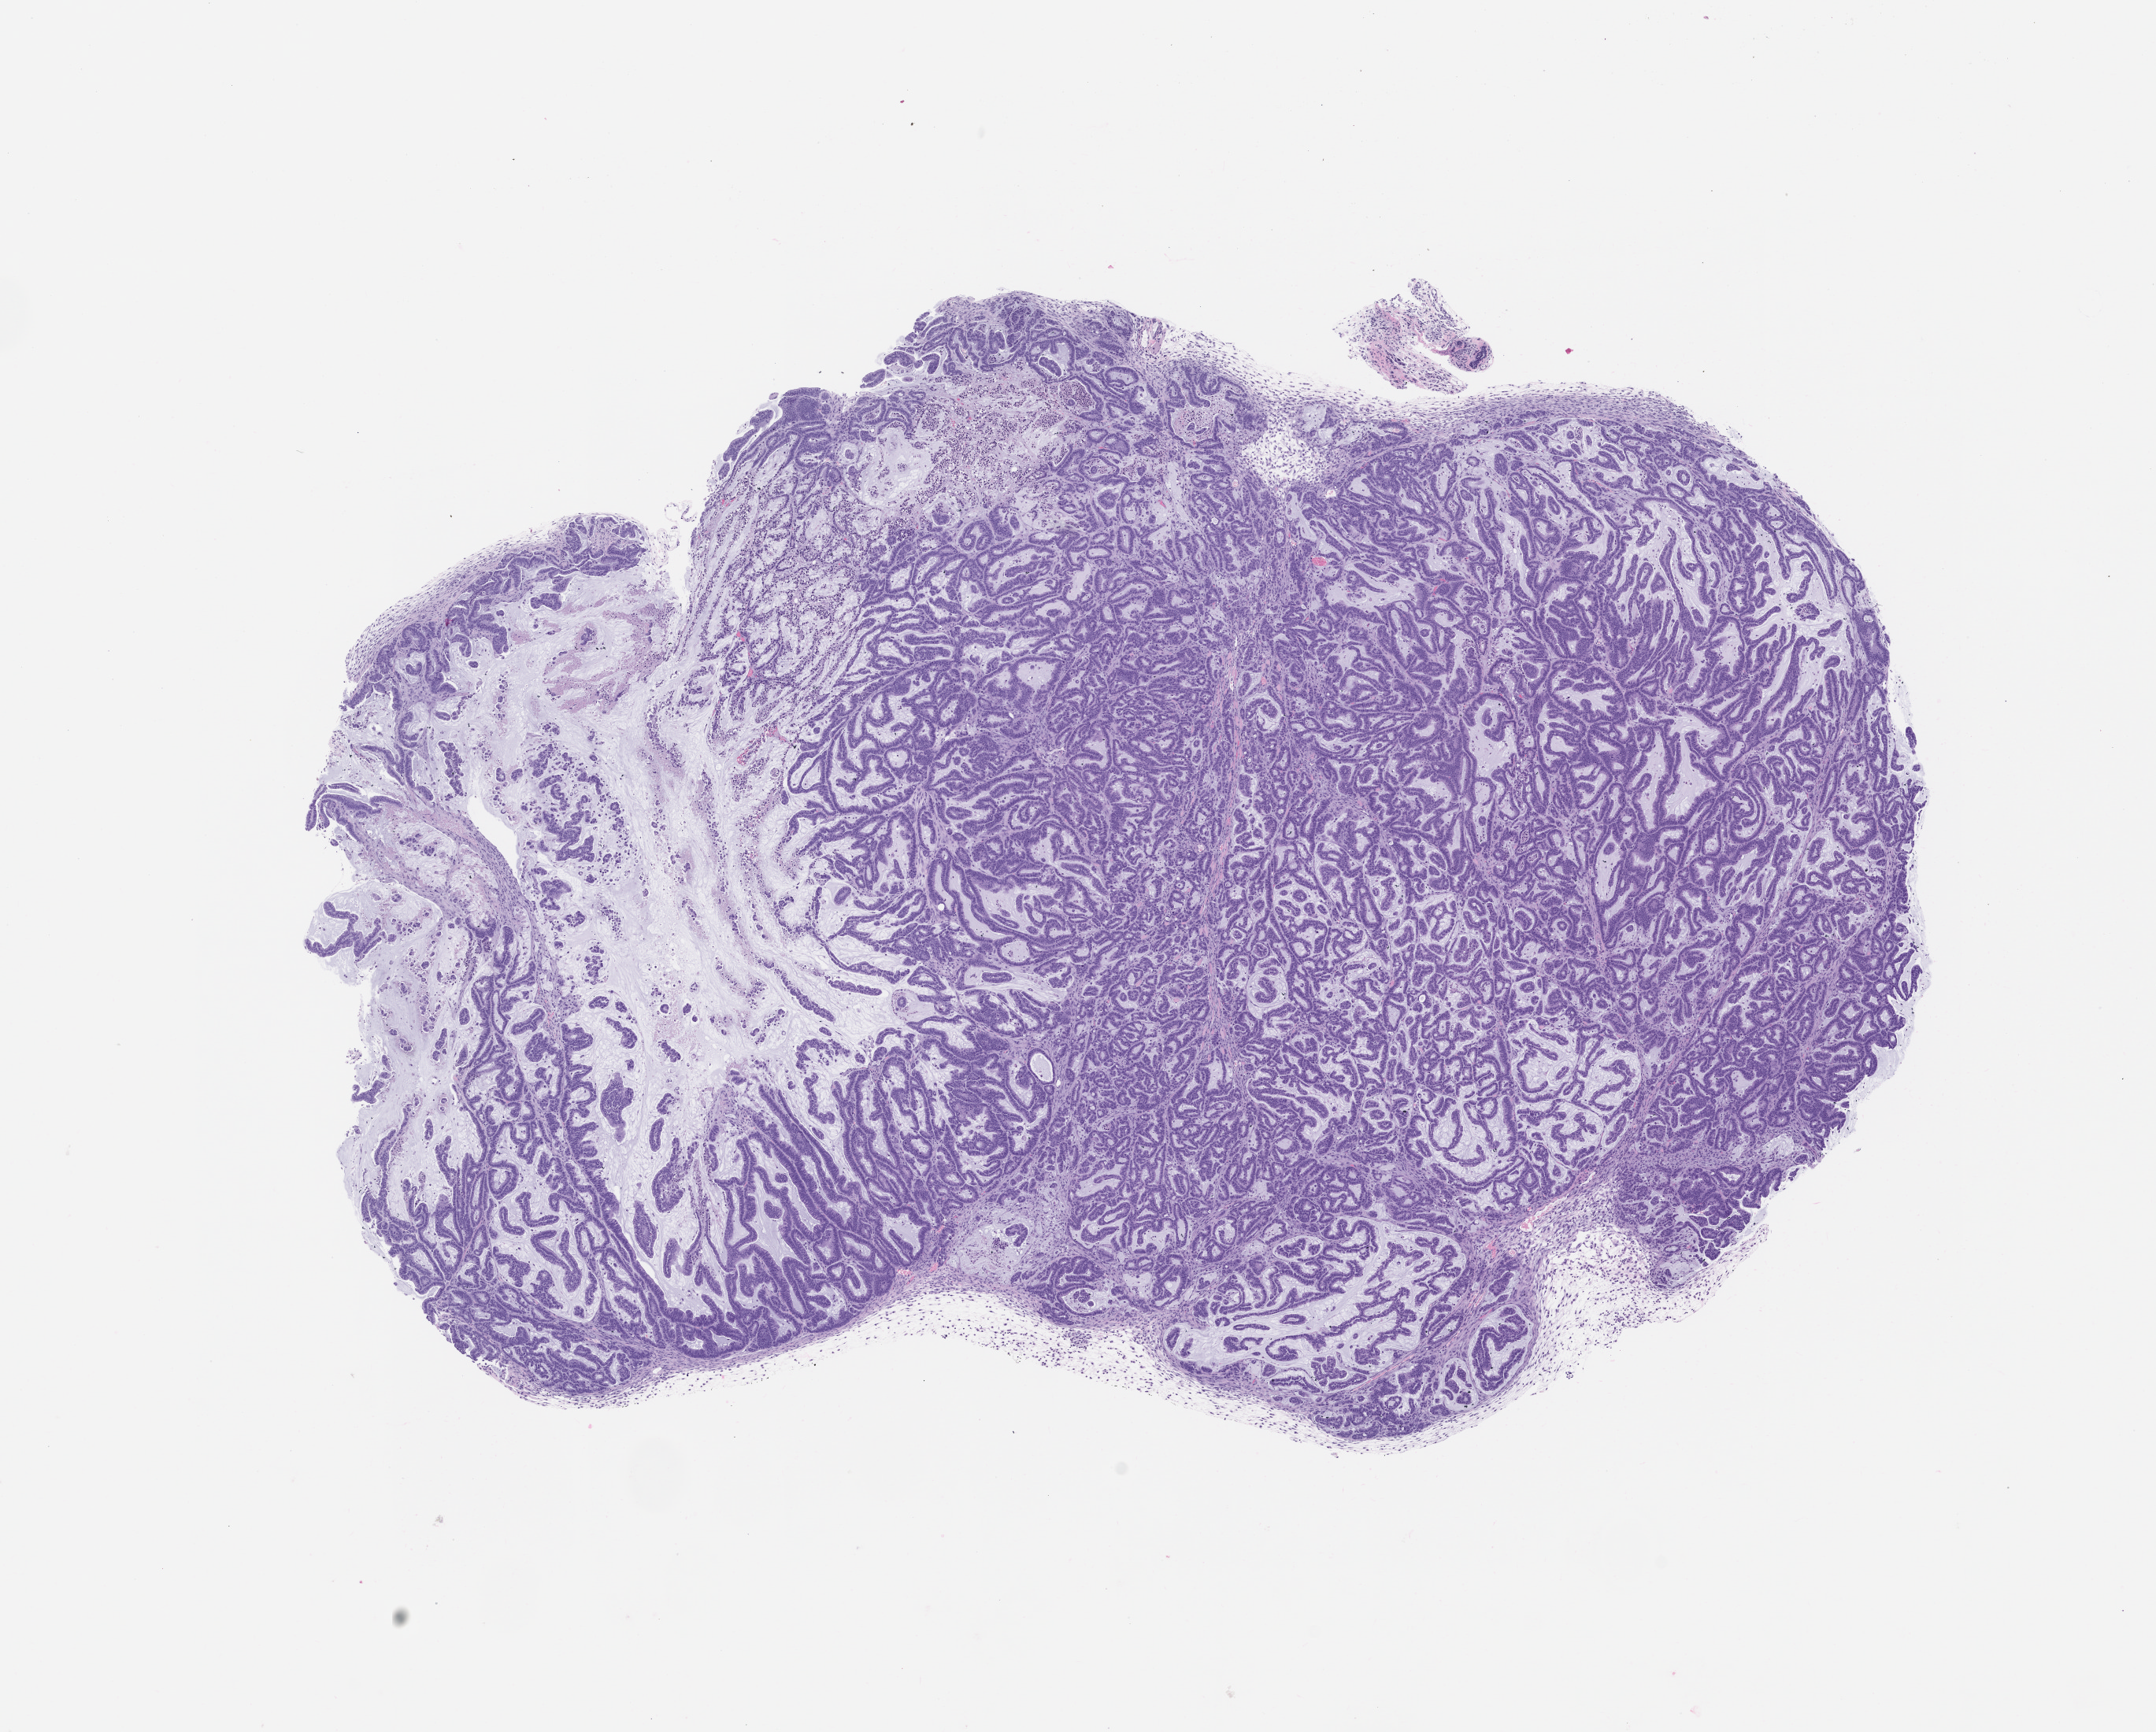
H&E whole-slide image of a patient-derived xenograft (PDX) tumor grown in a mouse, passage 0, shown as a low-resolution overview of the whole scanned area (about 11.0 x 8.8 mm). Formalin-fixed, paraffin-embedded (FFPE) tissue. Originating tumor site category: colon.
Originating patient diagnosis: Colon Adenocarcinoma.